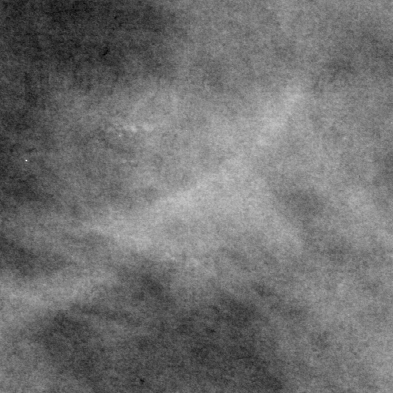
Crop from a digitized film mammogram around one marked abnormality, left breast, MLO view, BI-RADS breast density category 4 (scale 1–4).
Calcifications, morphology amorphous, distribution clustered; BI-RADS assessment category 4; subtlety rating 2 on a 1 (subtle) to 5 (obvious) scale; pathology (as recorded): benign.